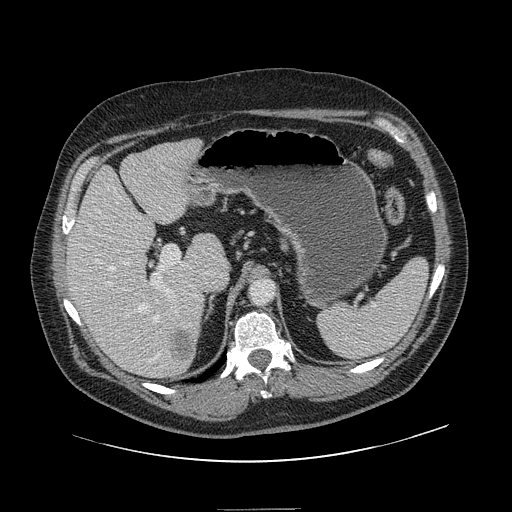
Contrast-enhanced abdominal CT, one axial slice; position 92 of 154 along the scan axis; intravenous contrast given; soft-tissue window (W 400 / L 40 HU); 2.5 mm slice thickness; 512 × 512 image matrix, field of view 451 × 451 mm. Male patient, age 61 years. From the clinical record (not read from this slice): diagnosis: colorectal cancer liver metastases, imaged before liver resection; multiple liver metastases: yes.
Structures marked on this image (outlined manually by an expert reader):
- hepatic veins: bounding box (x1, y1, x2, y2) in pixels: (89, 210, 178, 362)
- liver: (68, 140, 224, 378)
- planned liver remnant (the part of the liver to remain after resection): (68, 146, 224, 365)
- portal vein (with intrahepatic branches): (105, 186, 185, 297)
- liver metastasis: (174, 332, 196, 364)